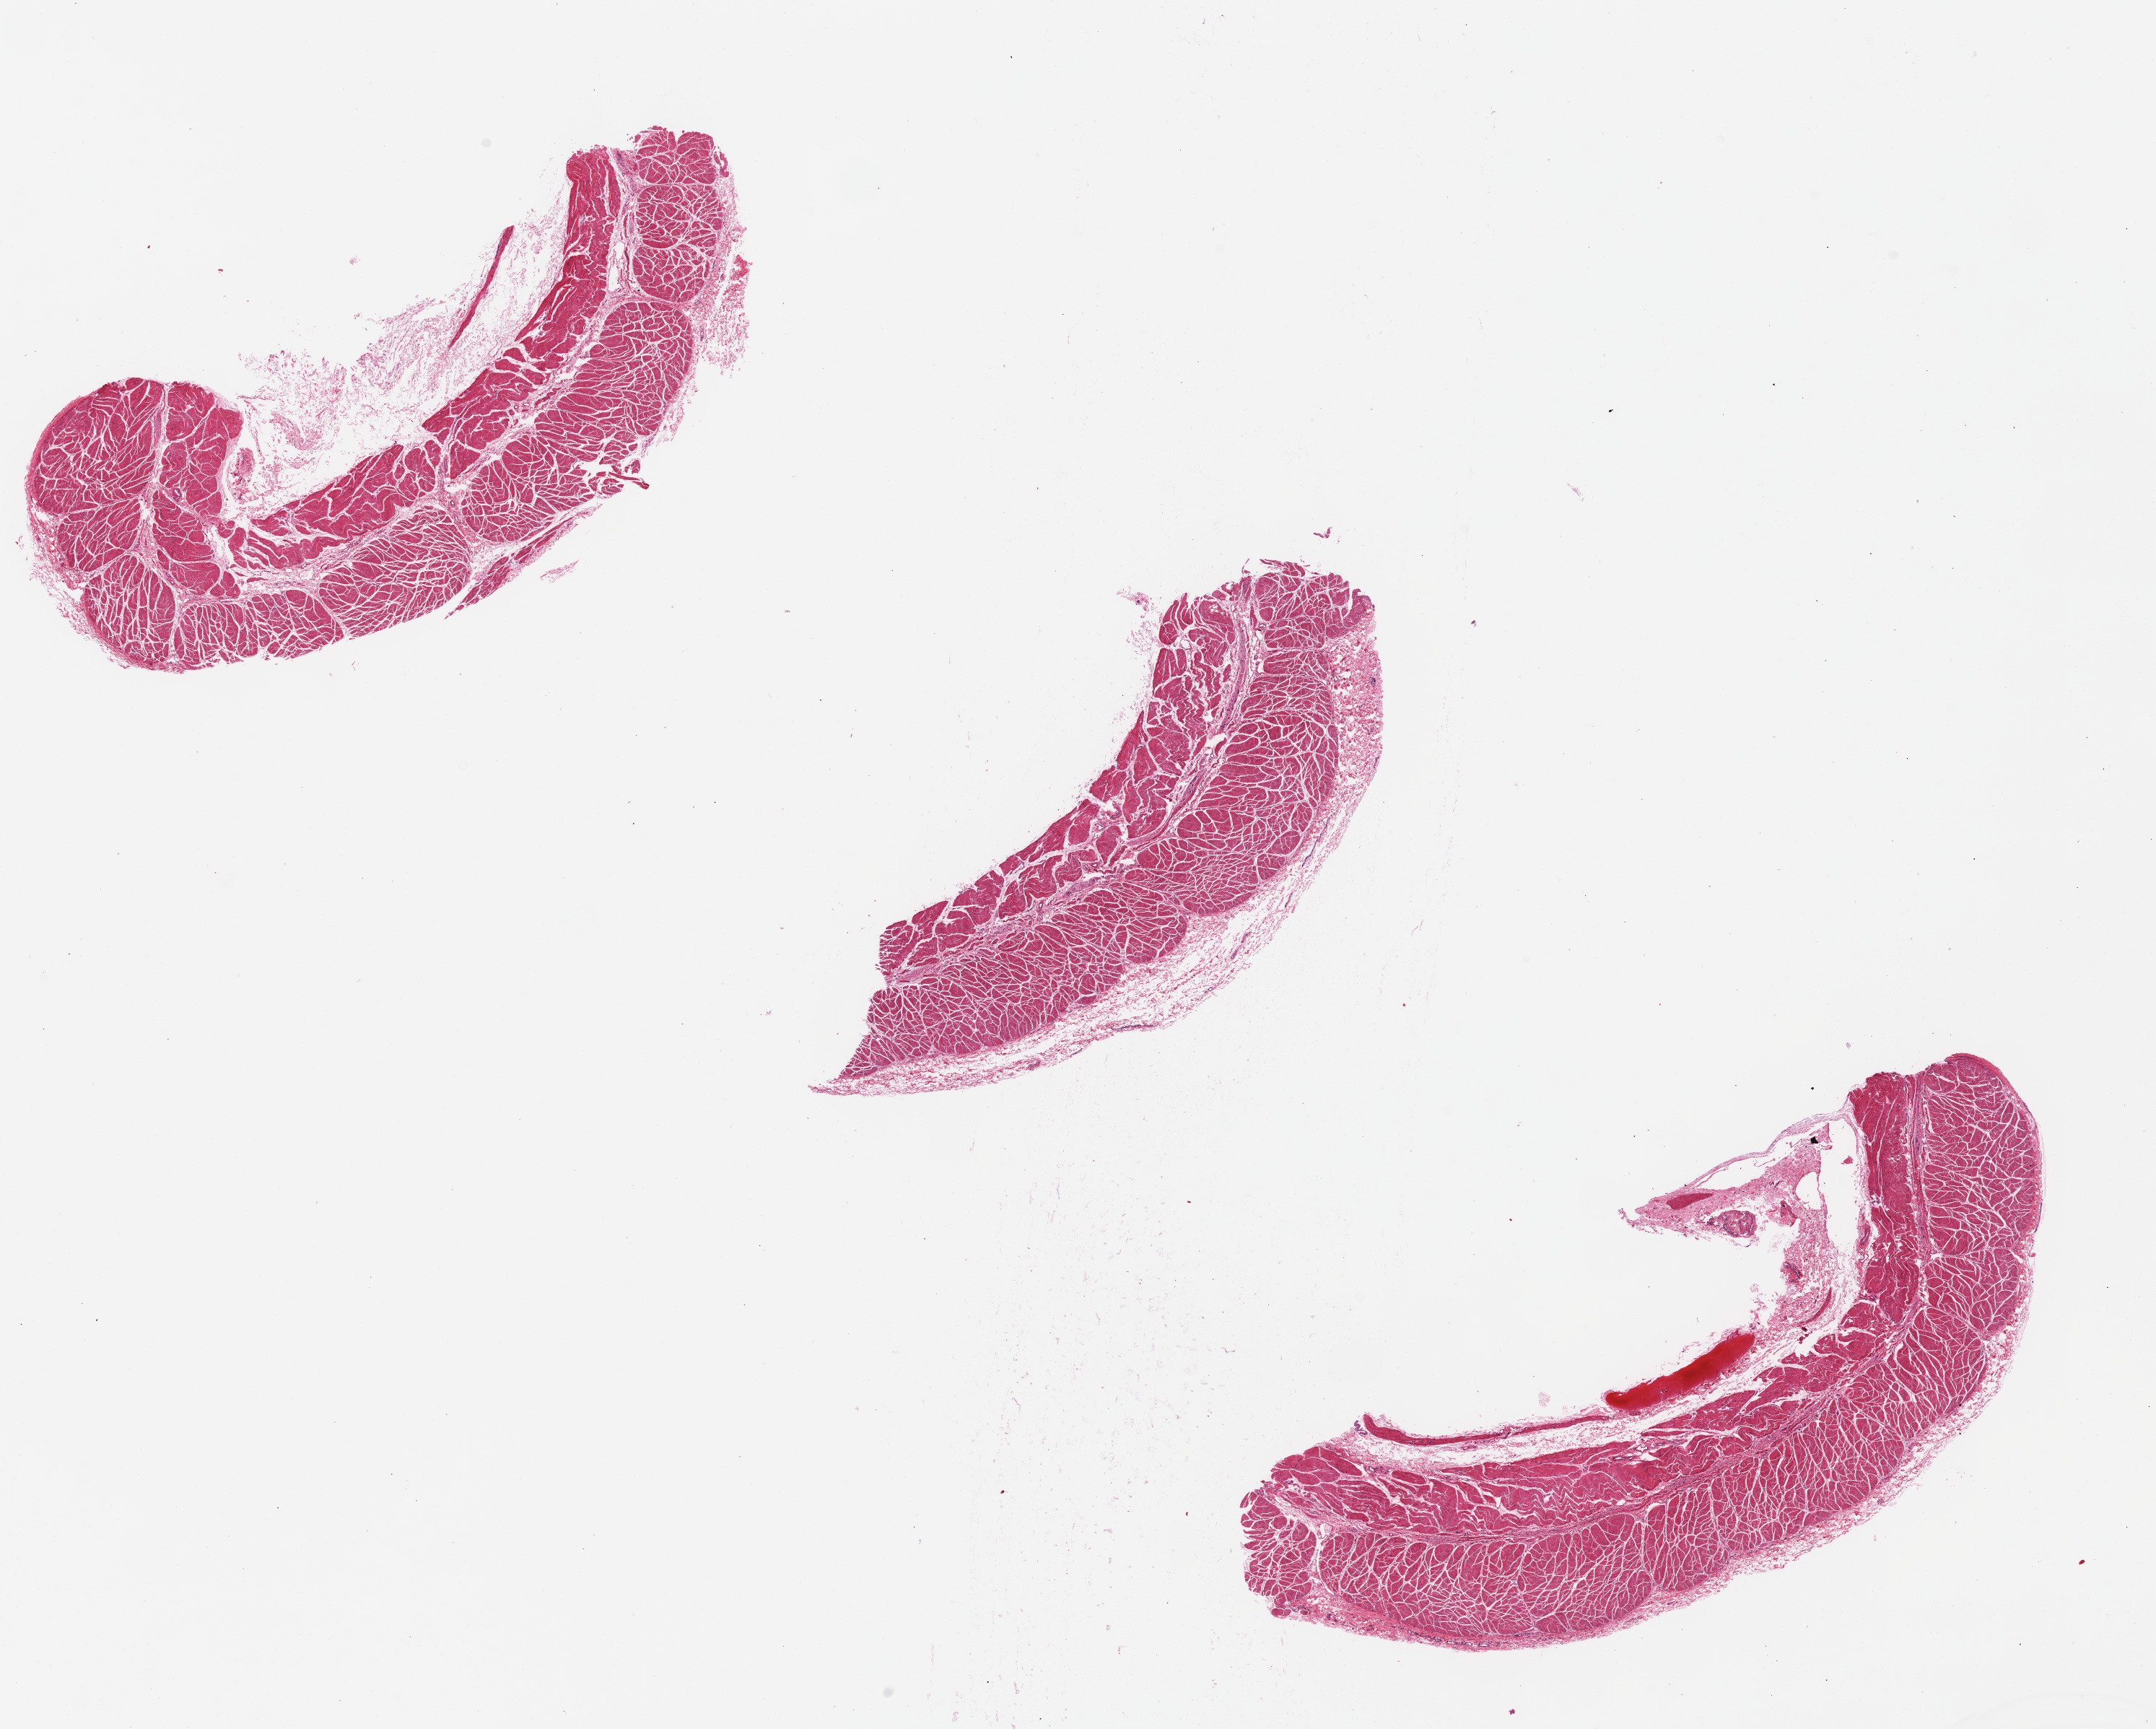
Digitized H&E-stained section, a low-resolution overview of the entire scanned area, about 23.6 x 18.9 mm; PAXgene-fixed paraffin-embedded (PFPE) section; sampled site (target tissue): esophageal muscle; tissue donor sample. Donor sex: male.
- review note (as recorded): 3 pieces